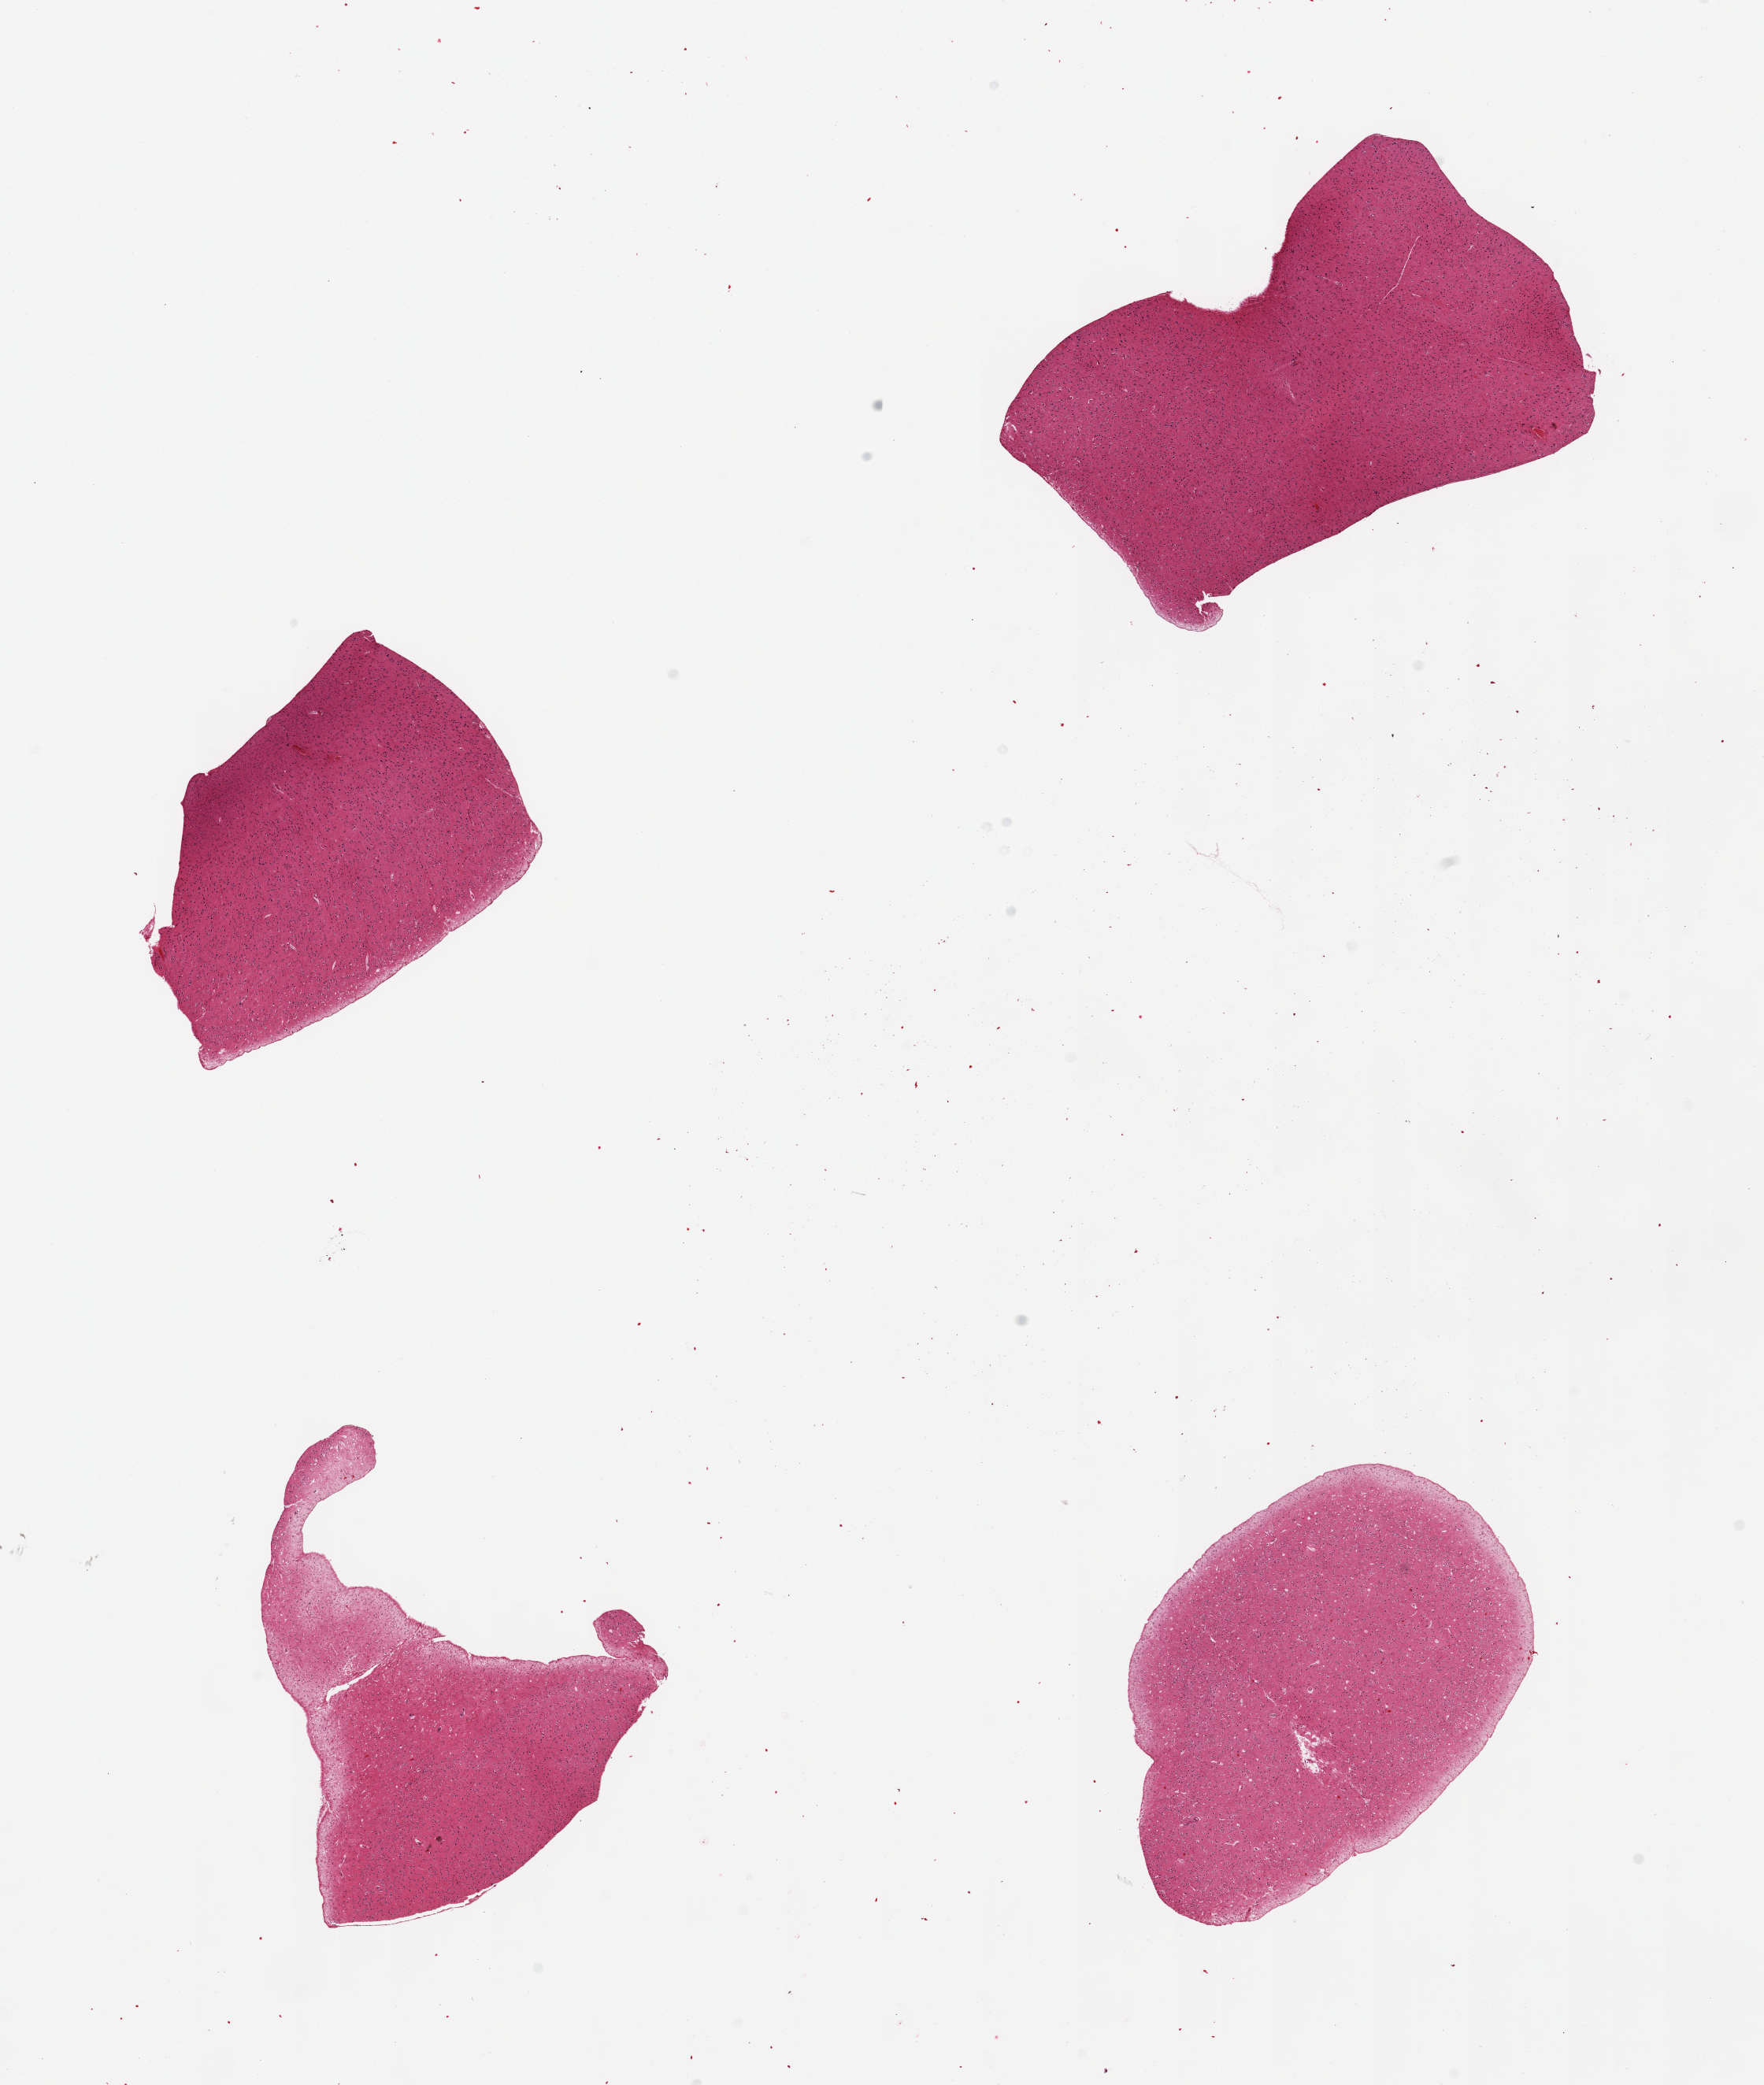
Whole-slide image, hematoxylin and eosin (H&E) stain — a low-resolution overview of the entire scanned area, about 17.7 x 20.9 mm. PAXgene-fixed paraffin-embedded (PFPE) section. Sampled site (target tissue): cerebral cortex. Tissue donor sample. Male donor.
- pathologist's review note for this sample: 4 pieces, no abnormalities